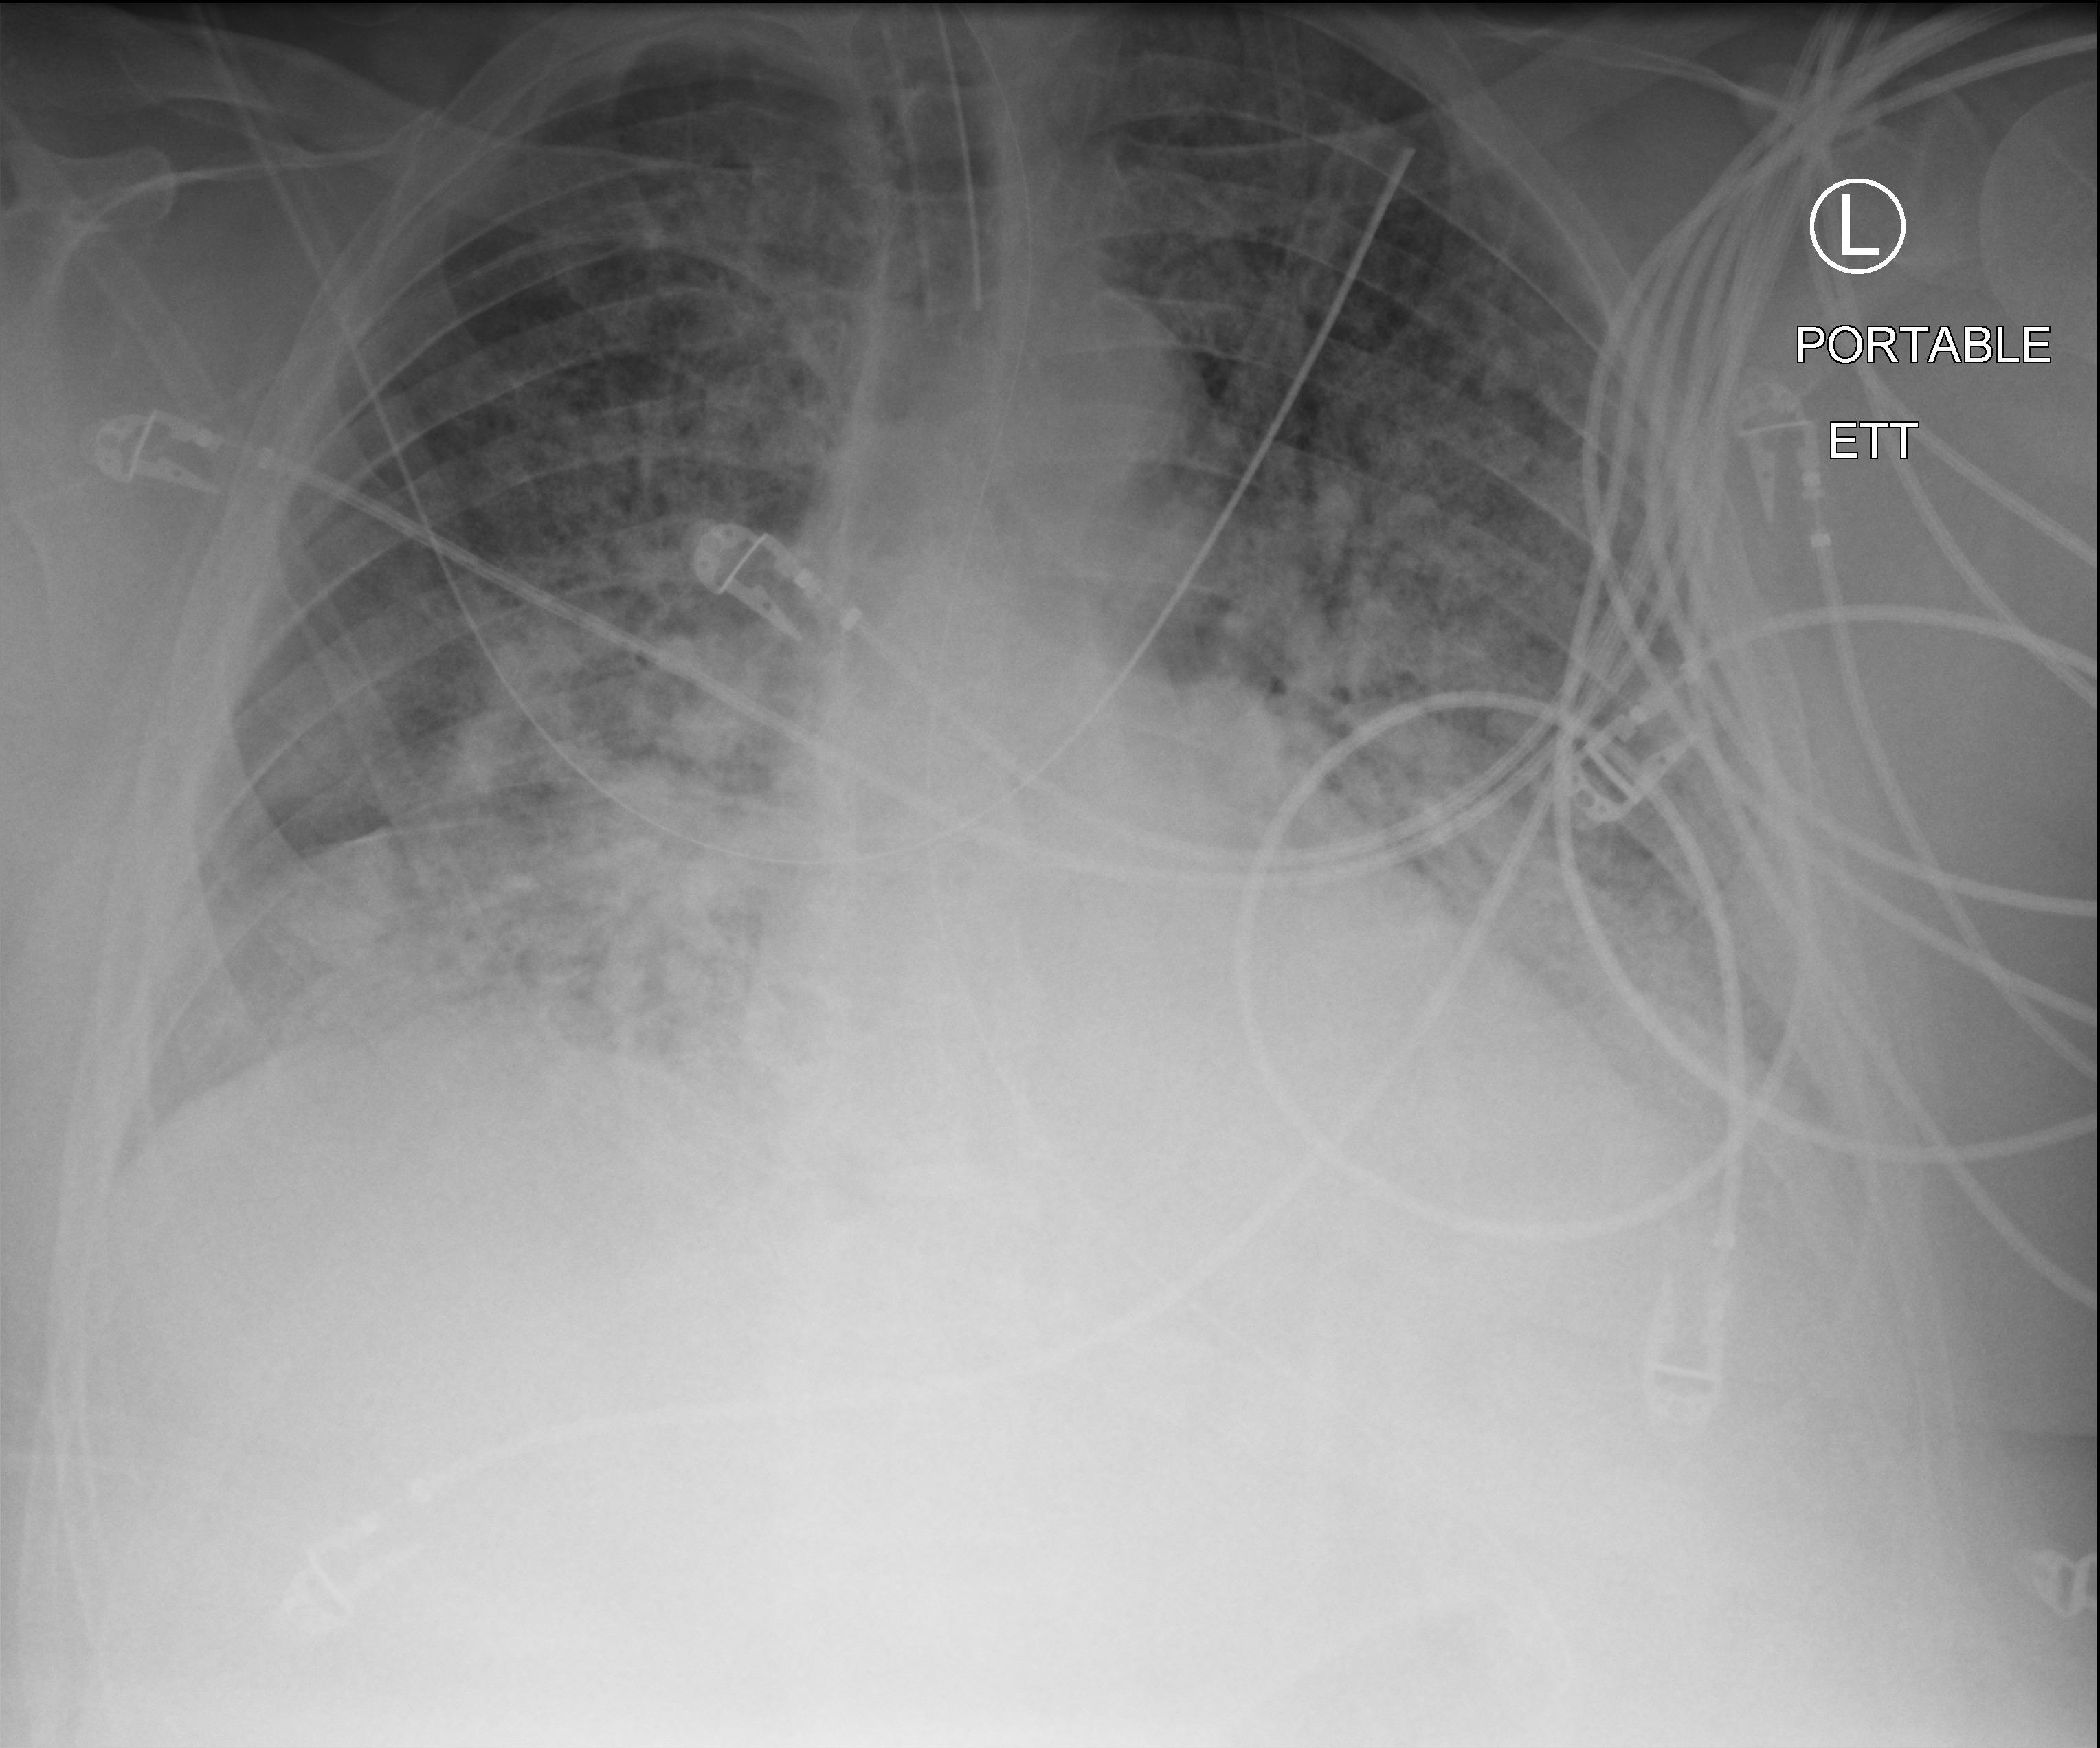
Chest X-ray (portable), anteroposterior (AP) projection. Male patient hospitalised with COVID-19, age 60–74 years.
Hospital-stay facts (about this admission, not read from this image; timing relative to this image not recorded): mechanically ventilated during this hospital stay: yes.